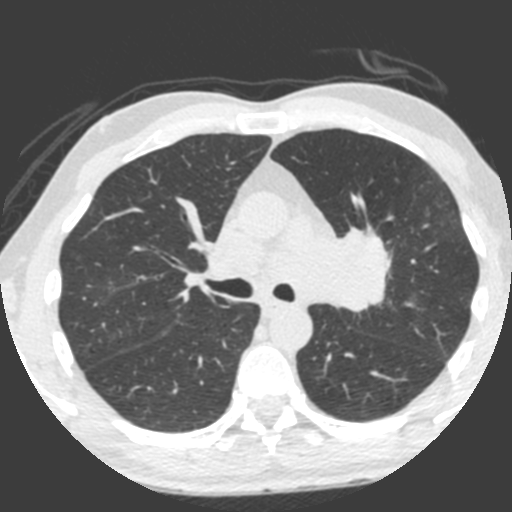
Low-dose screening chest CT, axial slice. Third screening round (two years after baseline). Lung window (W 1500 / L -600 HU). 2 mm slice thickness. Standard (soft-tissue) reconstruction kernel (B). Slice 139 of 212 in the series. Male, age 55 years at enrolment. Current smoker at enrolment.
Expert reader's lesion annotation, bounding box <309,221,396,324> (left, top, right, bottom; pixels). Reader record for this screening exam (exam-level; its link to the box is not recorded): non-calcified nodule or mass ≥4 mm, left upper lobe, 49 × 29 mm, spiculated (stellate) margins, soft tissue attenuation, pre-existing on the prior screen: yes; interval growth: yes. Official screen result: positive, other. Participant outcome: lung cancer diagnosed 0 days after this screen — small cell carcinoma, NOS, left upper lobe, undifferentiated (G4), stage IV (AJCC 6th edition), 60 mm at pathology.